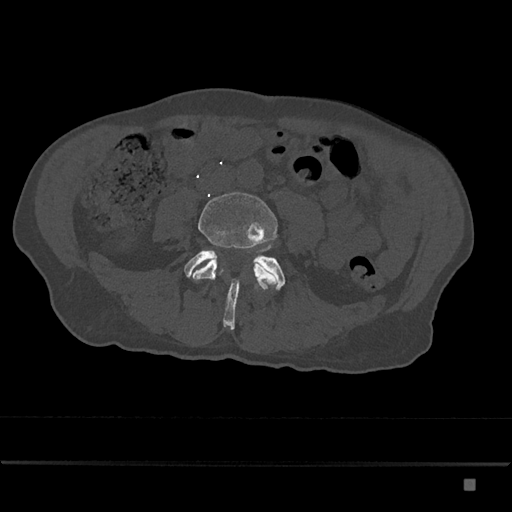
CT including the spine, one axial slice. Position 313 of 797 along the scan axis. Reconstruction kernel Br40s/3. Bone window (W 1800 / L 400 HU). 0.5 mm slice thickness. 512 × 512 image matrix, field of view 390 × 390 mm. Male patient, age 72 years. From the clinical record (not read from this slice): primary cancer: prostate.
Structures marked on this image (semi-automatic segmentation, software-assisted and operator-edited):
- L4 vertebra: bounding box [x1, y1, x2, y2] px = [190, 192, 278, 290]
- L5 vertebra: [184, 250, 286, 330]